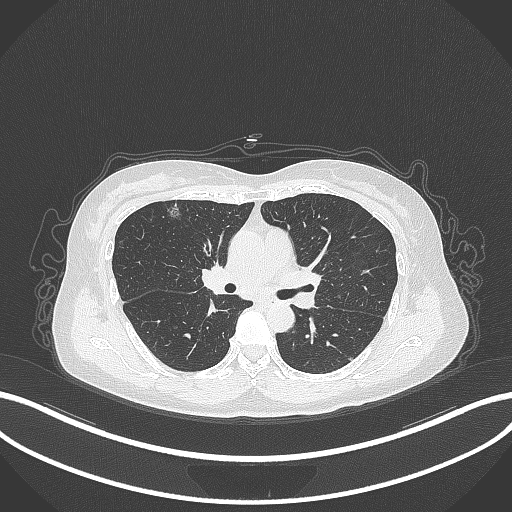
Chest CT, one axial slice. Slice 194 of 315 in the series (ordered by position). Reconstruction kernel B70f. Lung window (W 1500 / L -600 HU). 1 mm slice thickness. 512 × 512 image matrix, field of view 400 × 400 mm. Patient: female, 61 years. From the clinical record (not read from this slice): clinical TNM (as recorded): T1b N0 M0; histopathological grade: G1.
Annotated regions visible in this slice (bounding box drawn by a radiologist):
- lung tumour (recorded histology: adenocarcinoma): bounding box [x1, y1, x2, y2] px = [165, 200, 186, 221]